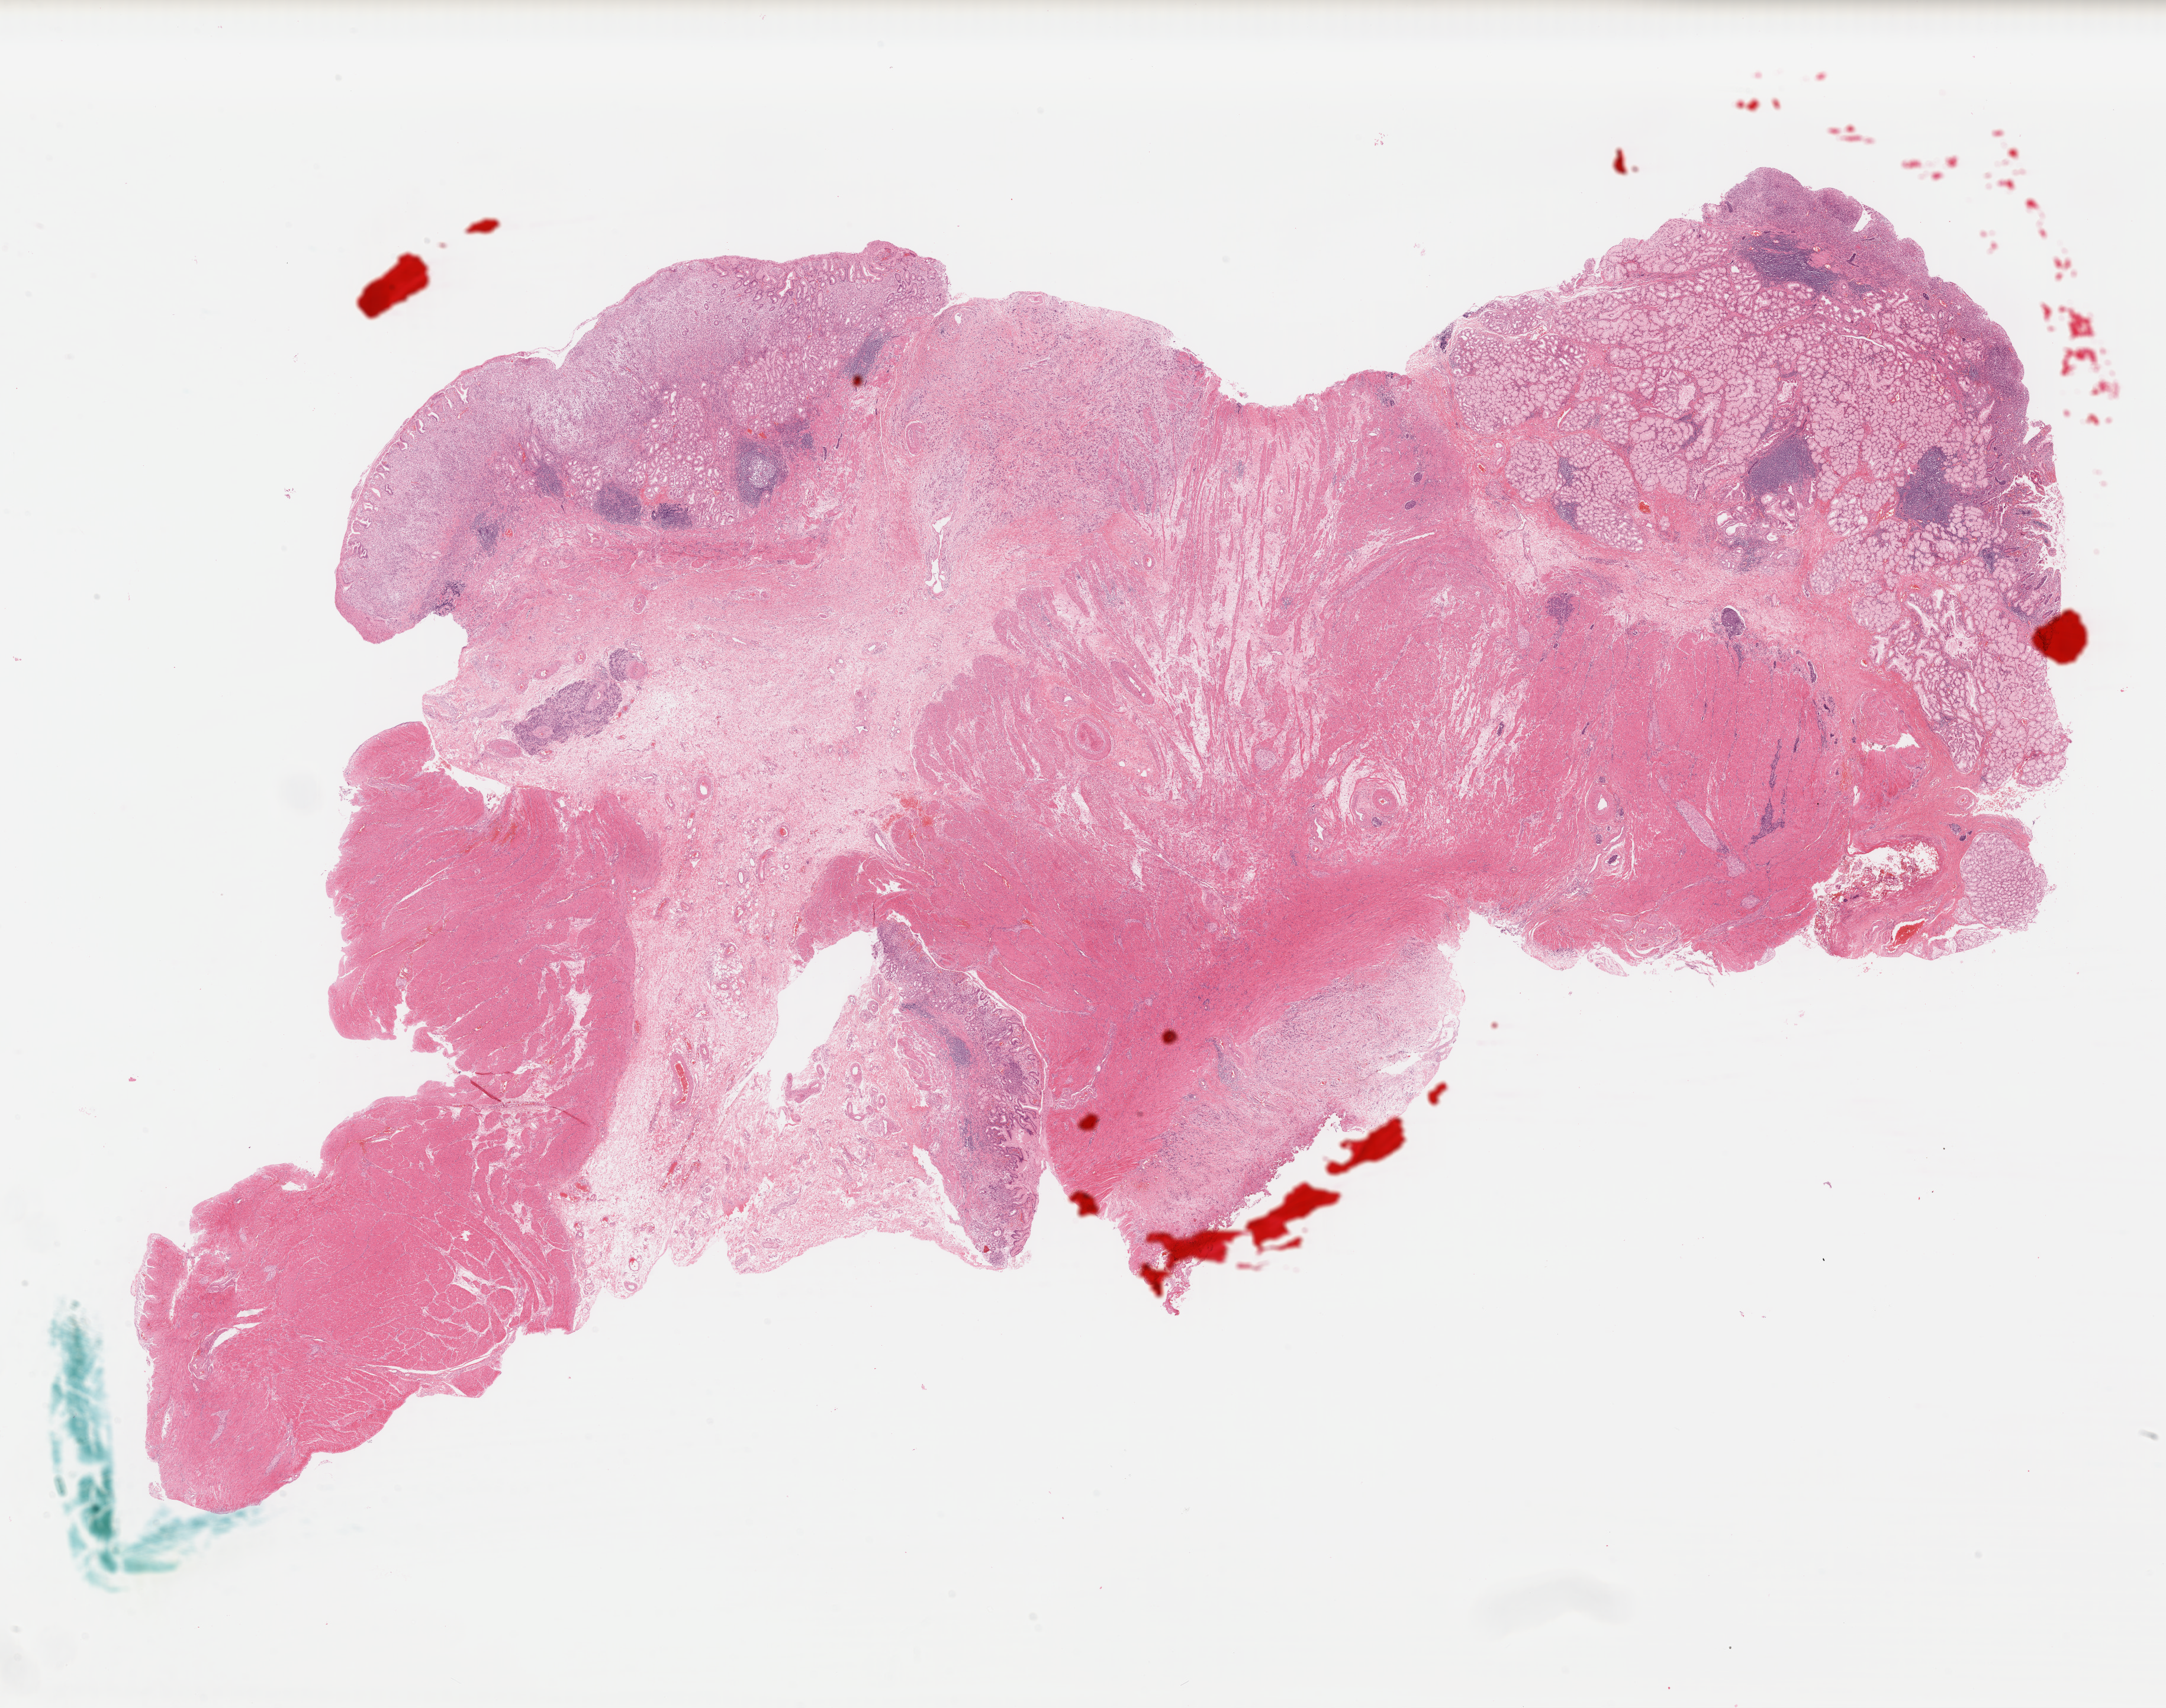
H&E whole-slide image, a low-resolution overview of the entire scanned area, about 28.8 x 22.7 mm (from a 40x scan); FFPE section; primary tumour sample from the stomach. Patient: male, age at initial diagnosis 51 years.
Pathologic diagnosis: Signet ring cell carcinoma.